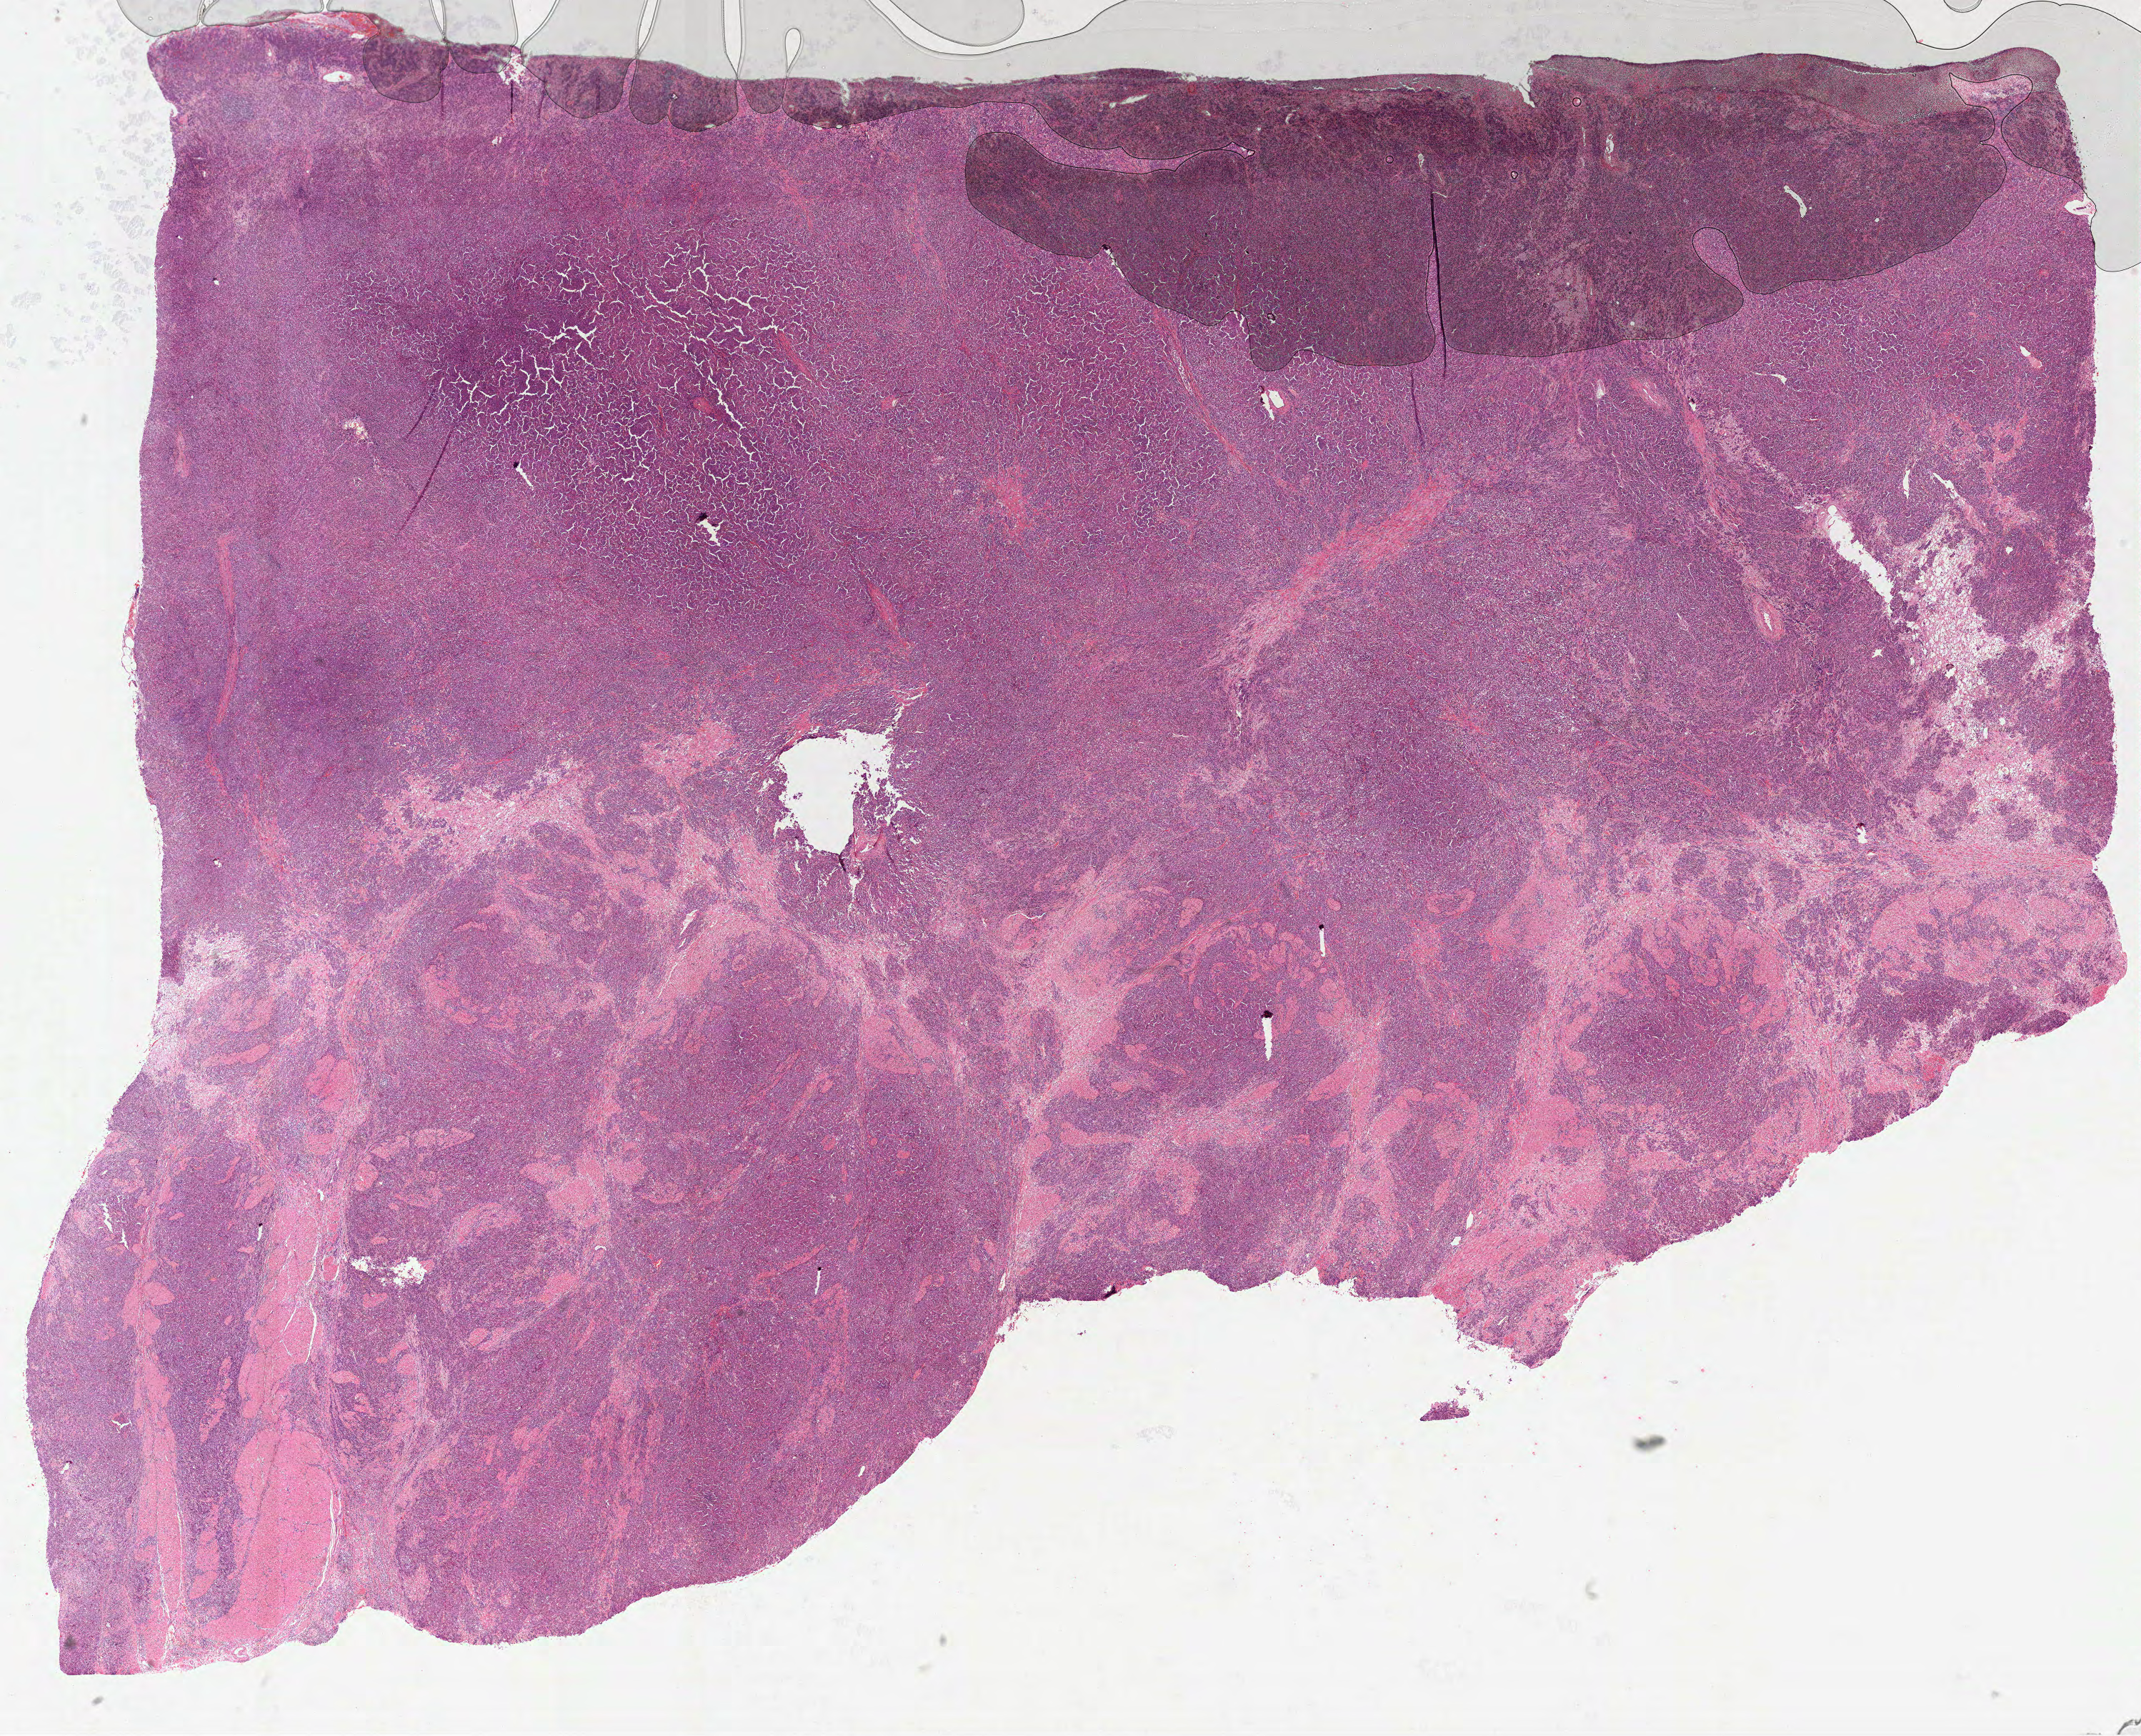
Whole-slide histology image, H&E, low-resolution overview of the scanned area, about 24.2 x 19.6 mm (slide scanned at 40x); FFPE section; primary tumour sample from the stomach. Patient: female, age at initial diagnosis 71 years. Histologic grade: G3 (poorly differentiated).
* lymph nodes positive (case pathology): 6 of 10 examined
* AJCC pathologic stage: IIIC (7th edition)
* diagnosis: Adenocarcinoma, NOS (fundus of stomach)
* TNM: T4b N2 M0